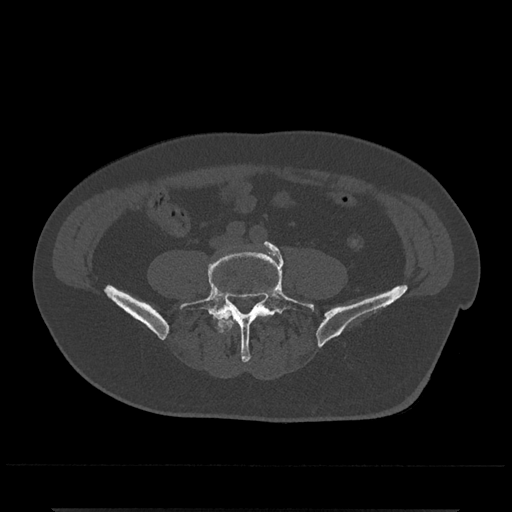
CT including the spine, one axial slice; slice 98 of 797 in the series (ordered by position); reconstruction kernel Br40s/3; bone window (W 1800 / L 400 HU); 512 × 512 image matrix, field of view 393 × 393 mm. Male patient, age 67 years. From the clinical record (not read from this slice): primary cancer: prostate.
Outlined on this slice (semi-automatic segmentation, software-assisted and operator-edited):
- L4 vertebra: bounding box <219,313,263,332> (left, top, right, bottom; pixels)
- L5 vertebra: <179,242,315,362>